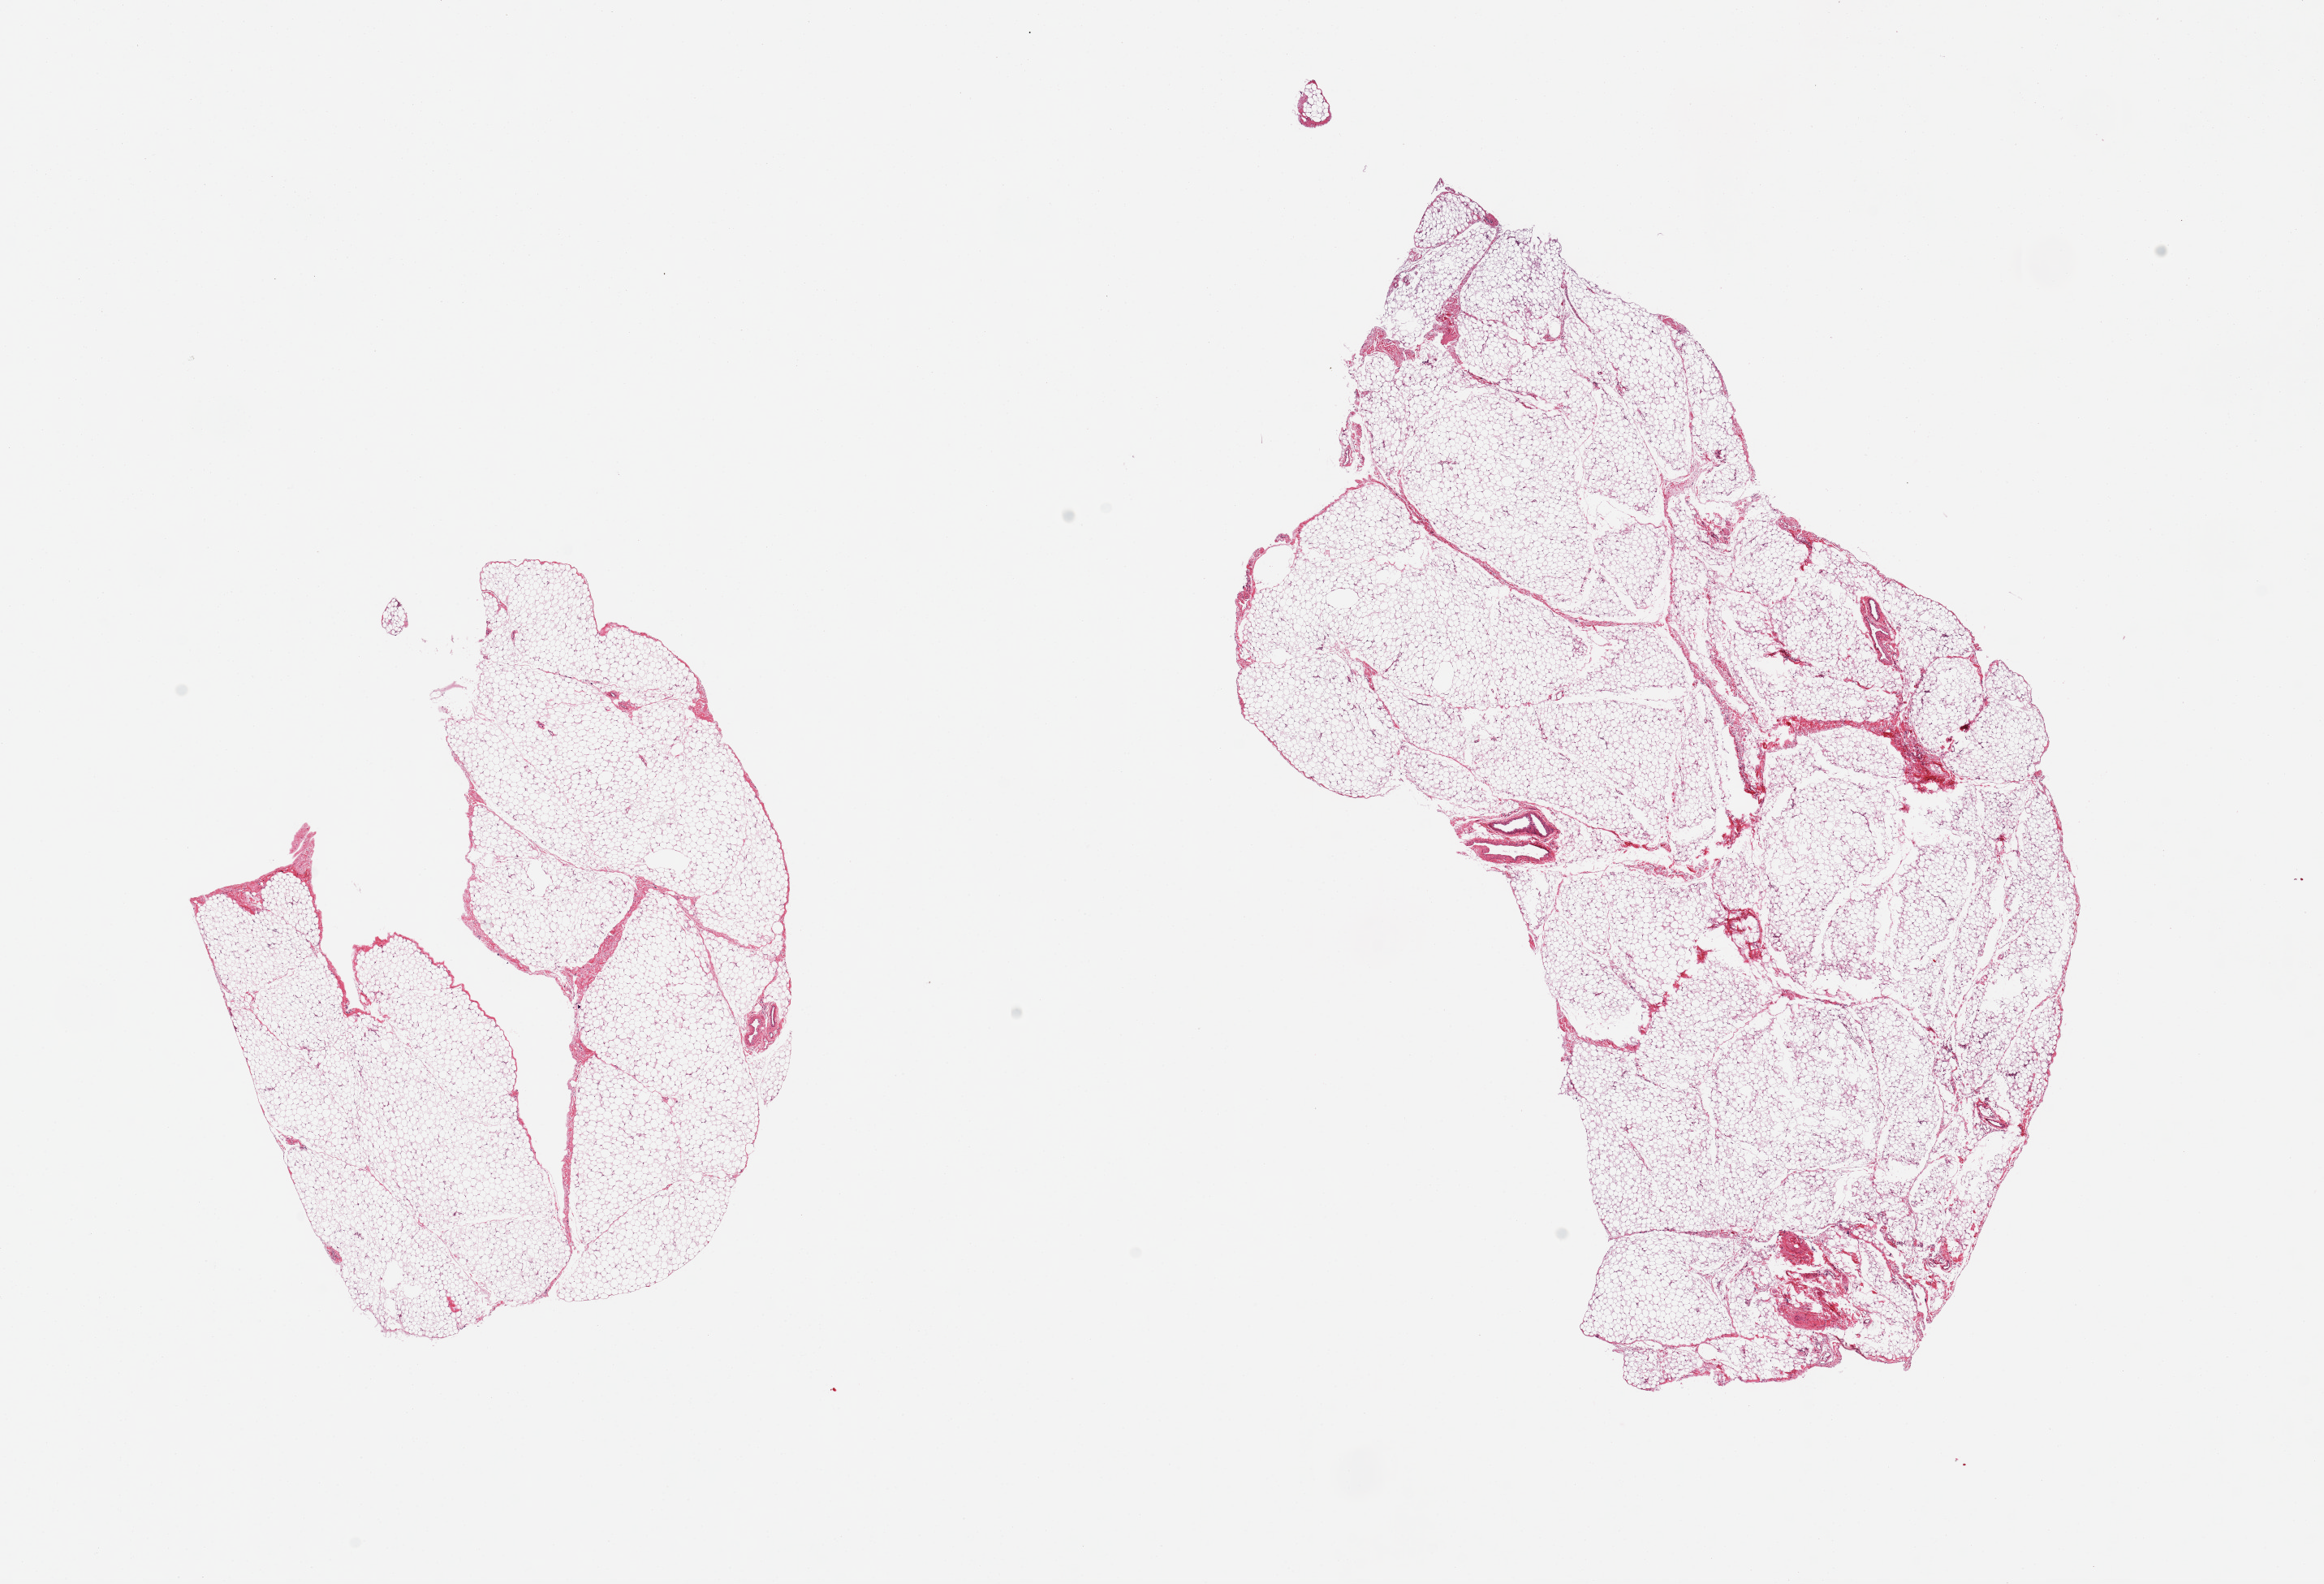
Hematoxylin and eosin (H&E) whole-slide image — shown as a low-resolution overview of the whole scanned area (about 22.6 x 15.4 mm, acquisition: 20x scan); PAXgene-fixed, paraffin-embedded tissue; sampled site (target tissue): omentum; tissue donor sample. Female donor.
Reviewer comment on this tissue sample: 2 pieces.